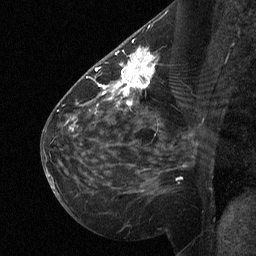
Breast MRI (dynamic contrast-enhanced), one sagittal slice. Slice 33 of 64 in the series (ordered by position). Dynamic contrast-enhanced study with each time point stored as its own series, time point 2 of 3 at this slice position (early post-contrast, ordered by acquisition time). 1.5 T. TE 4.8 ms, TR 27 ms. 256 × 256 image matrix, field of view 200 × 200 mm. Patient: female, 51 years. From the clinical record (not read from this slice): setting: breast cancer imaged before/during neoadjuvant chemotherapy; receptor status: HR-positive, HER2-negative.
Outlined on this slice (semi-automatically segmented with operator editing):
- analysis volume of interest (the breast-tissue region the enhancement analysis was run in; not a lesion): bounding box <112,46,156,106> (left, top, right, bottom; pixels)
- tumour enhancement mask (voxels above the 90 % enhancement threshold inside the analysis volume of interest): <112,49,153,105>